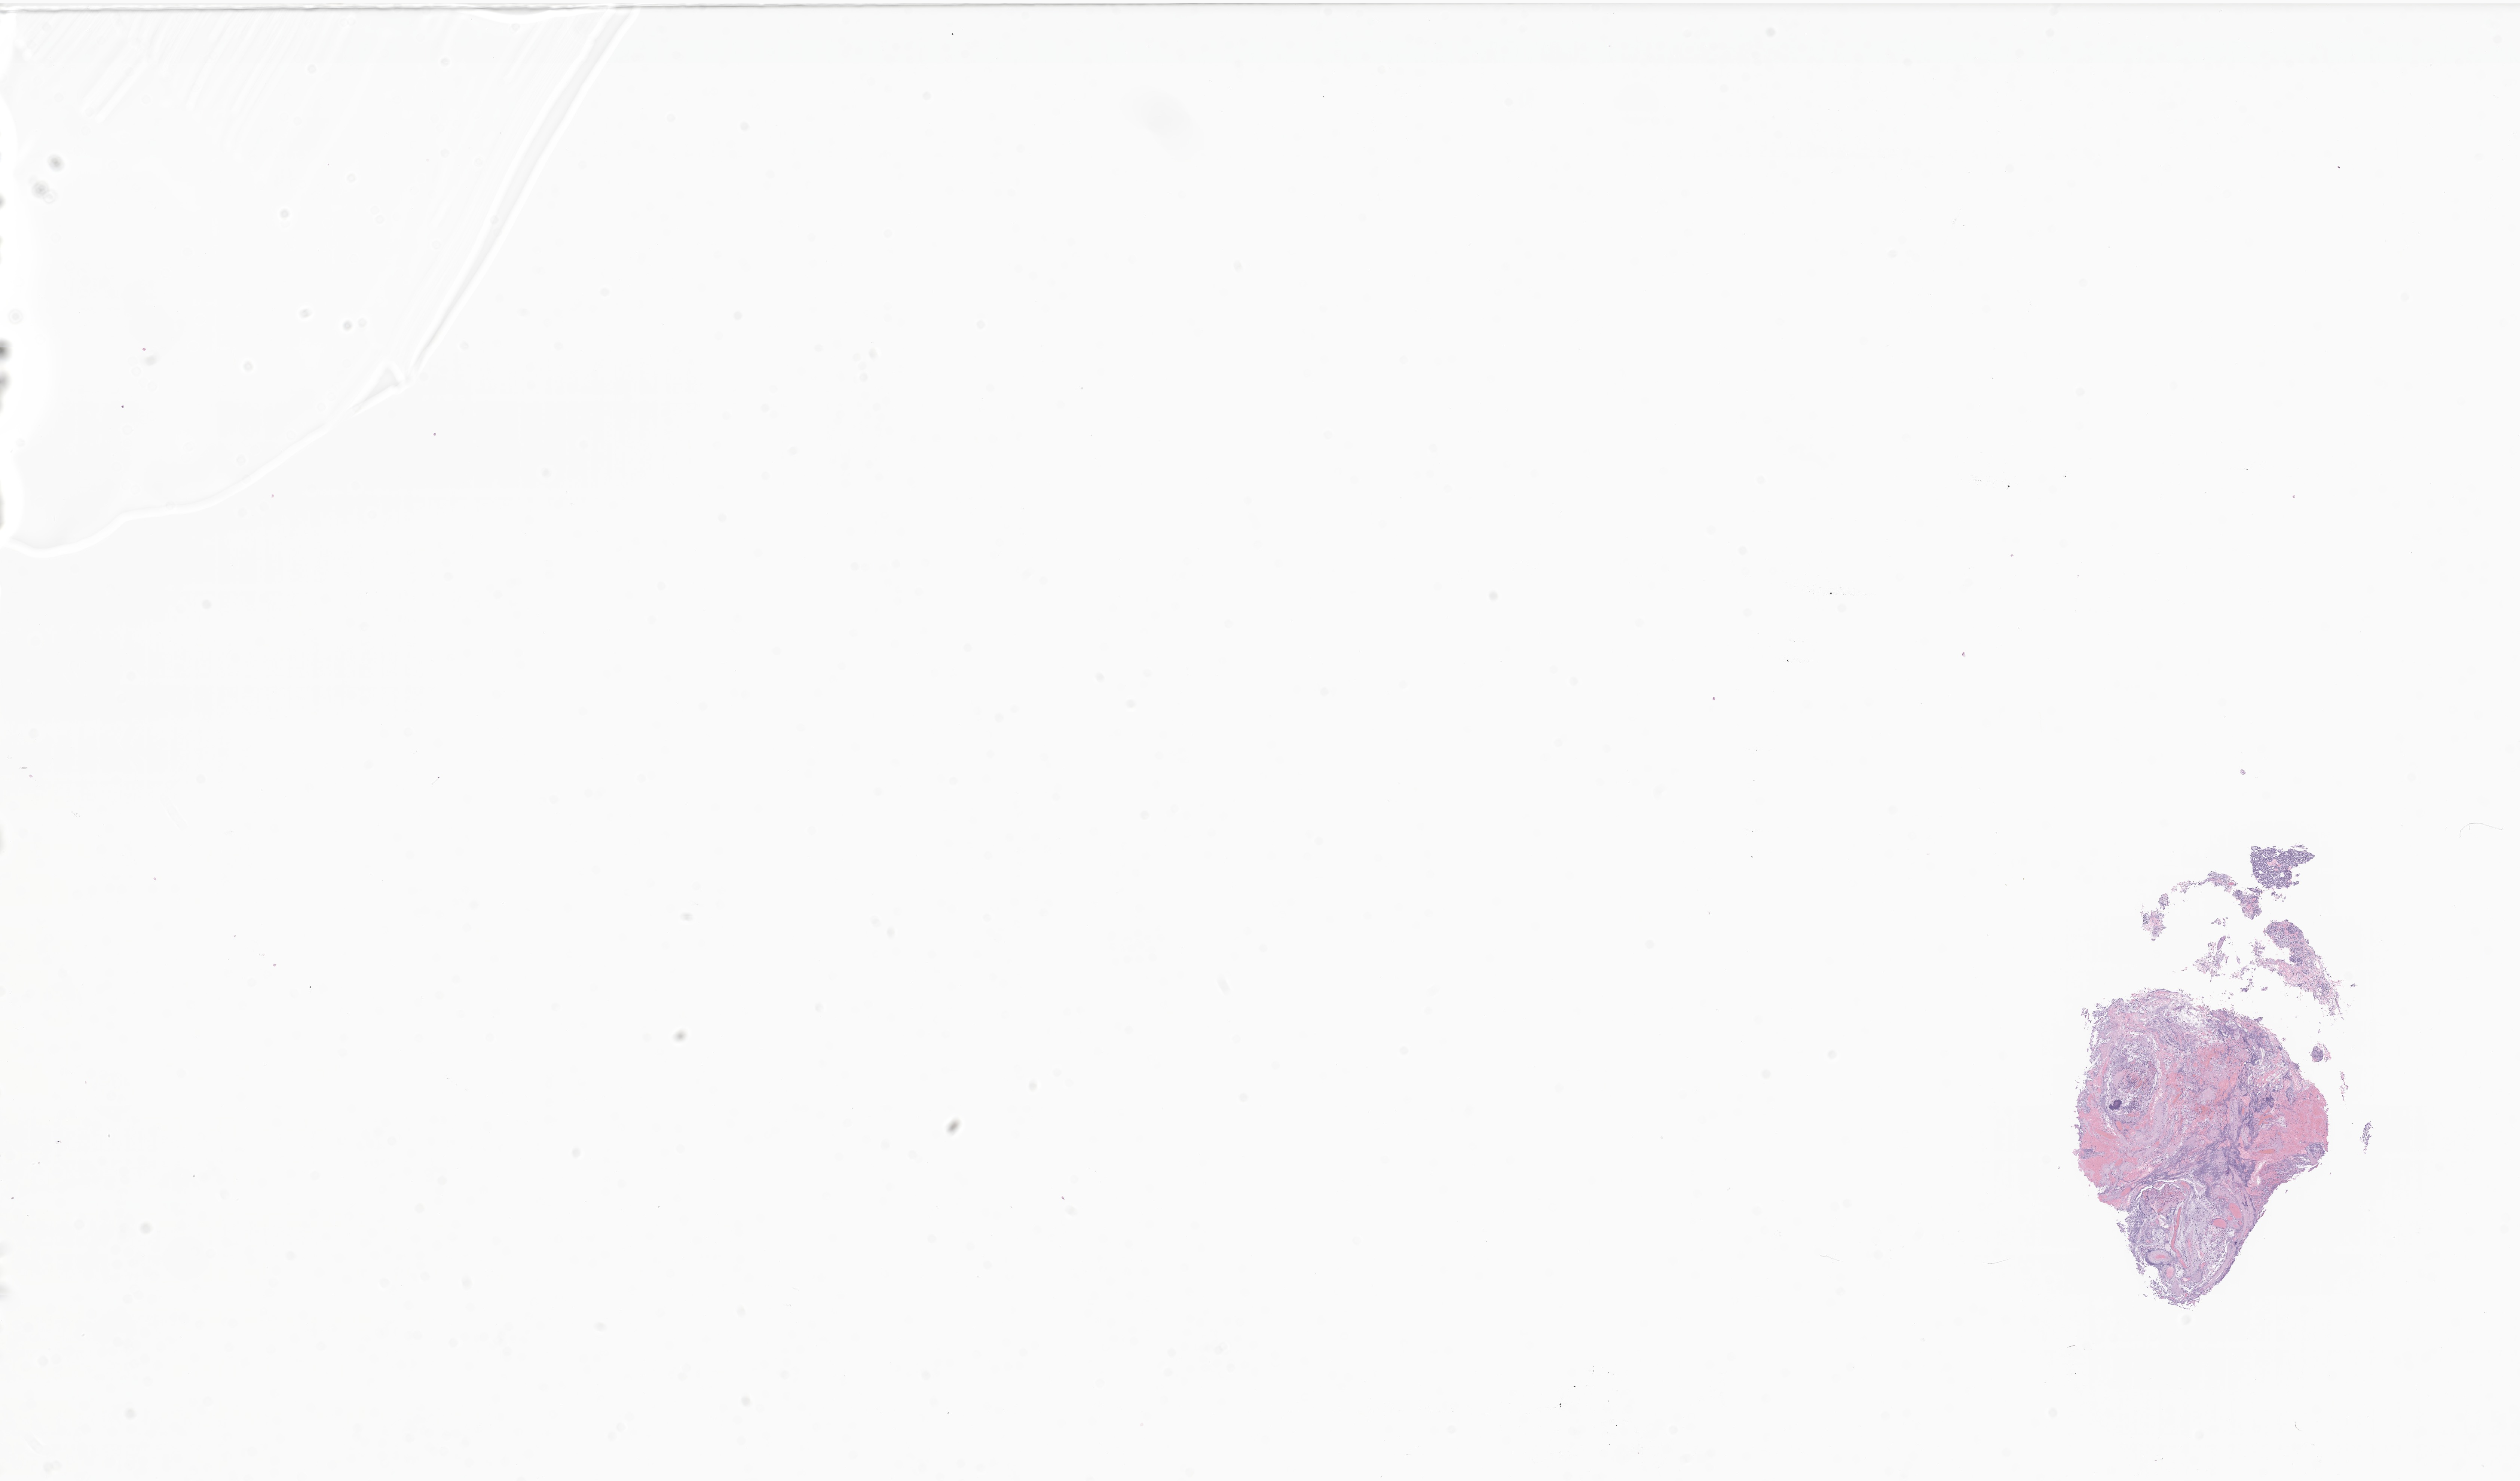
H&E whole-slide image of tumor tissue from the brain — a low-resolution overview of the entire scanned area, about 28.4 x 16.7 mm; FFPE section. Patient: female, age 228 months.
Diagnosis (ICD-O-3 morphology term): Medulloblastoma, NOS.